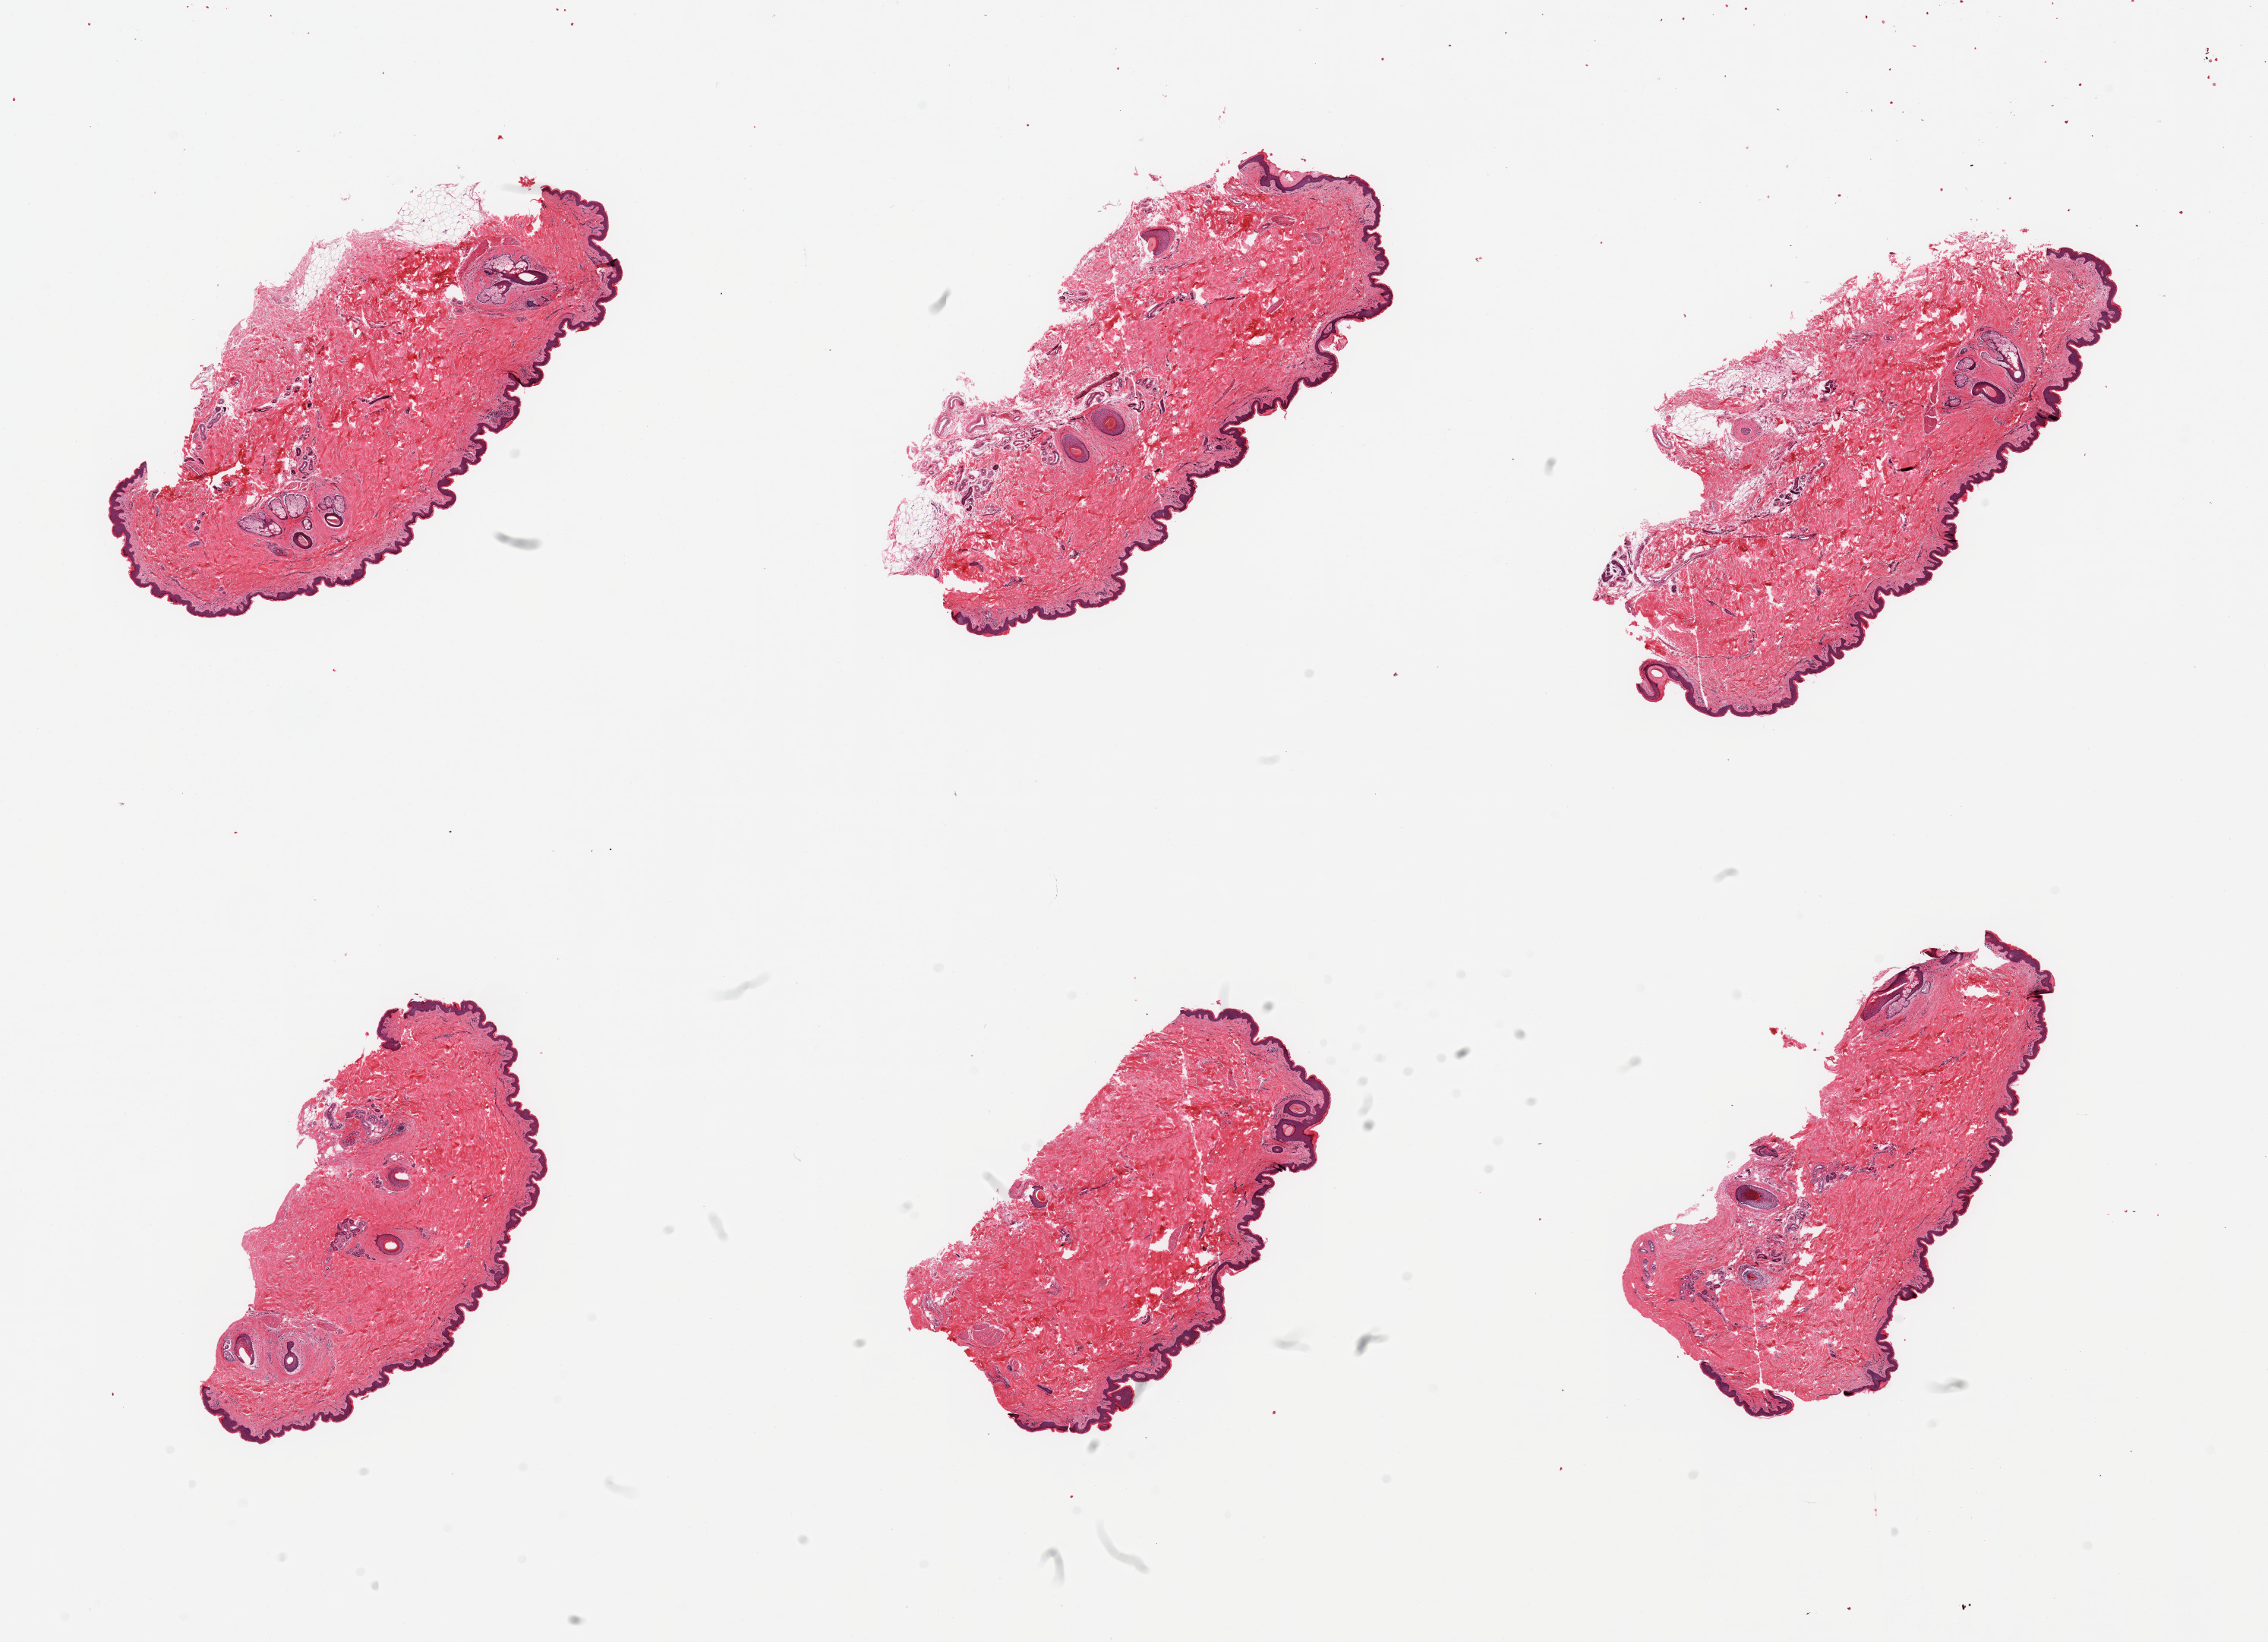
H&E whole-slide image, brightfield, shown as a low-resolution overview of the whole scanned area (about 23.6 x 17.1 mm, from a 20x scan); PAXgene-fixed, paraffin-embedded tissue; sampled site (target tissue): skin of suprapubic region; donor tissue sample. Donor sex: male.
- review note (as recorded): 6 pieces, trace dermal fat; squamous epithelium is is ~40-50 microns